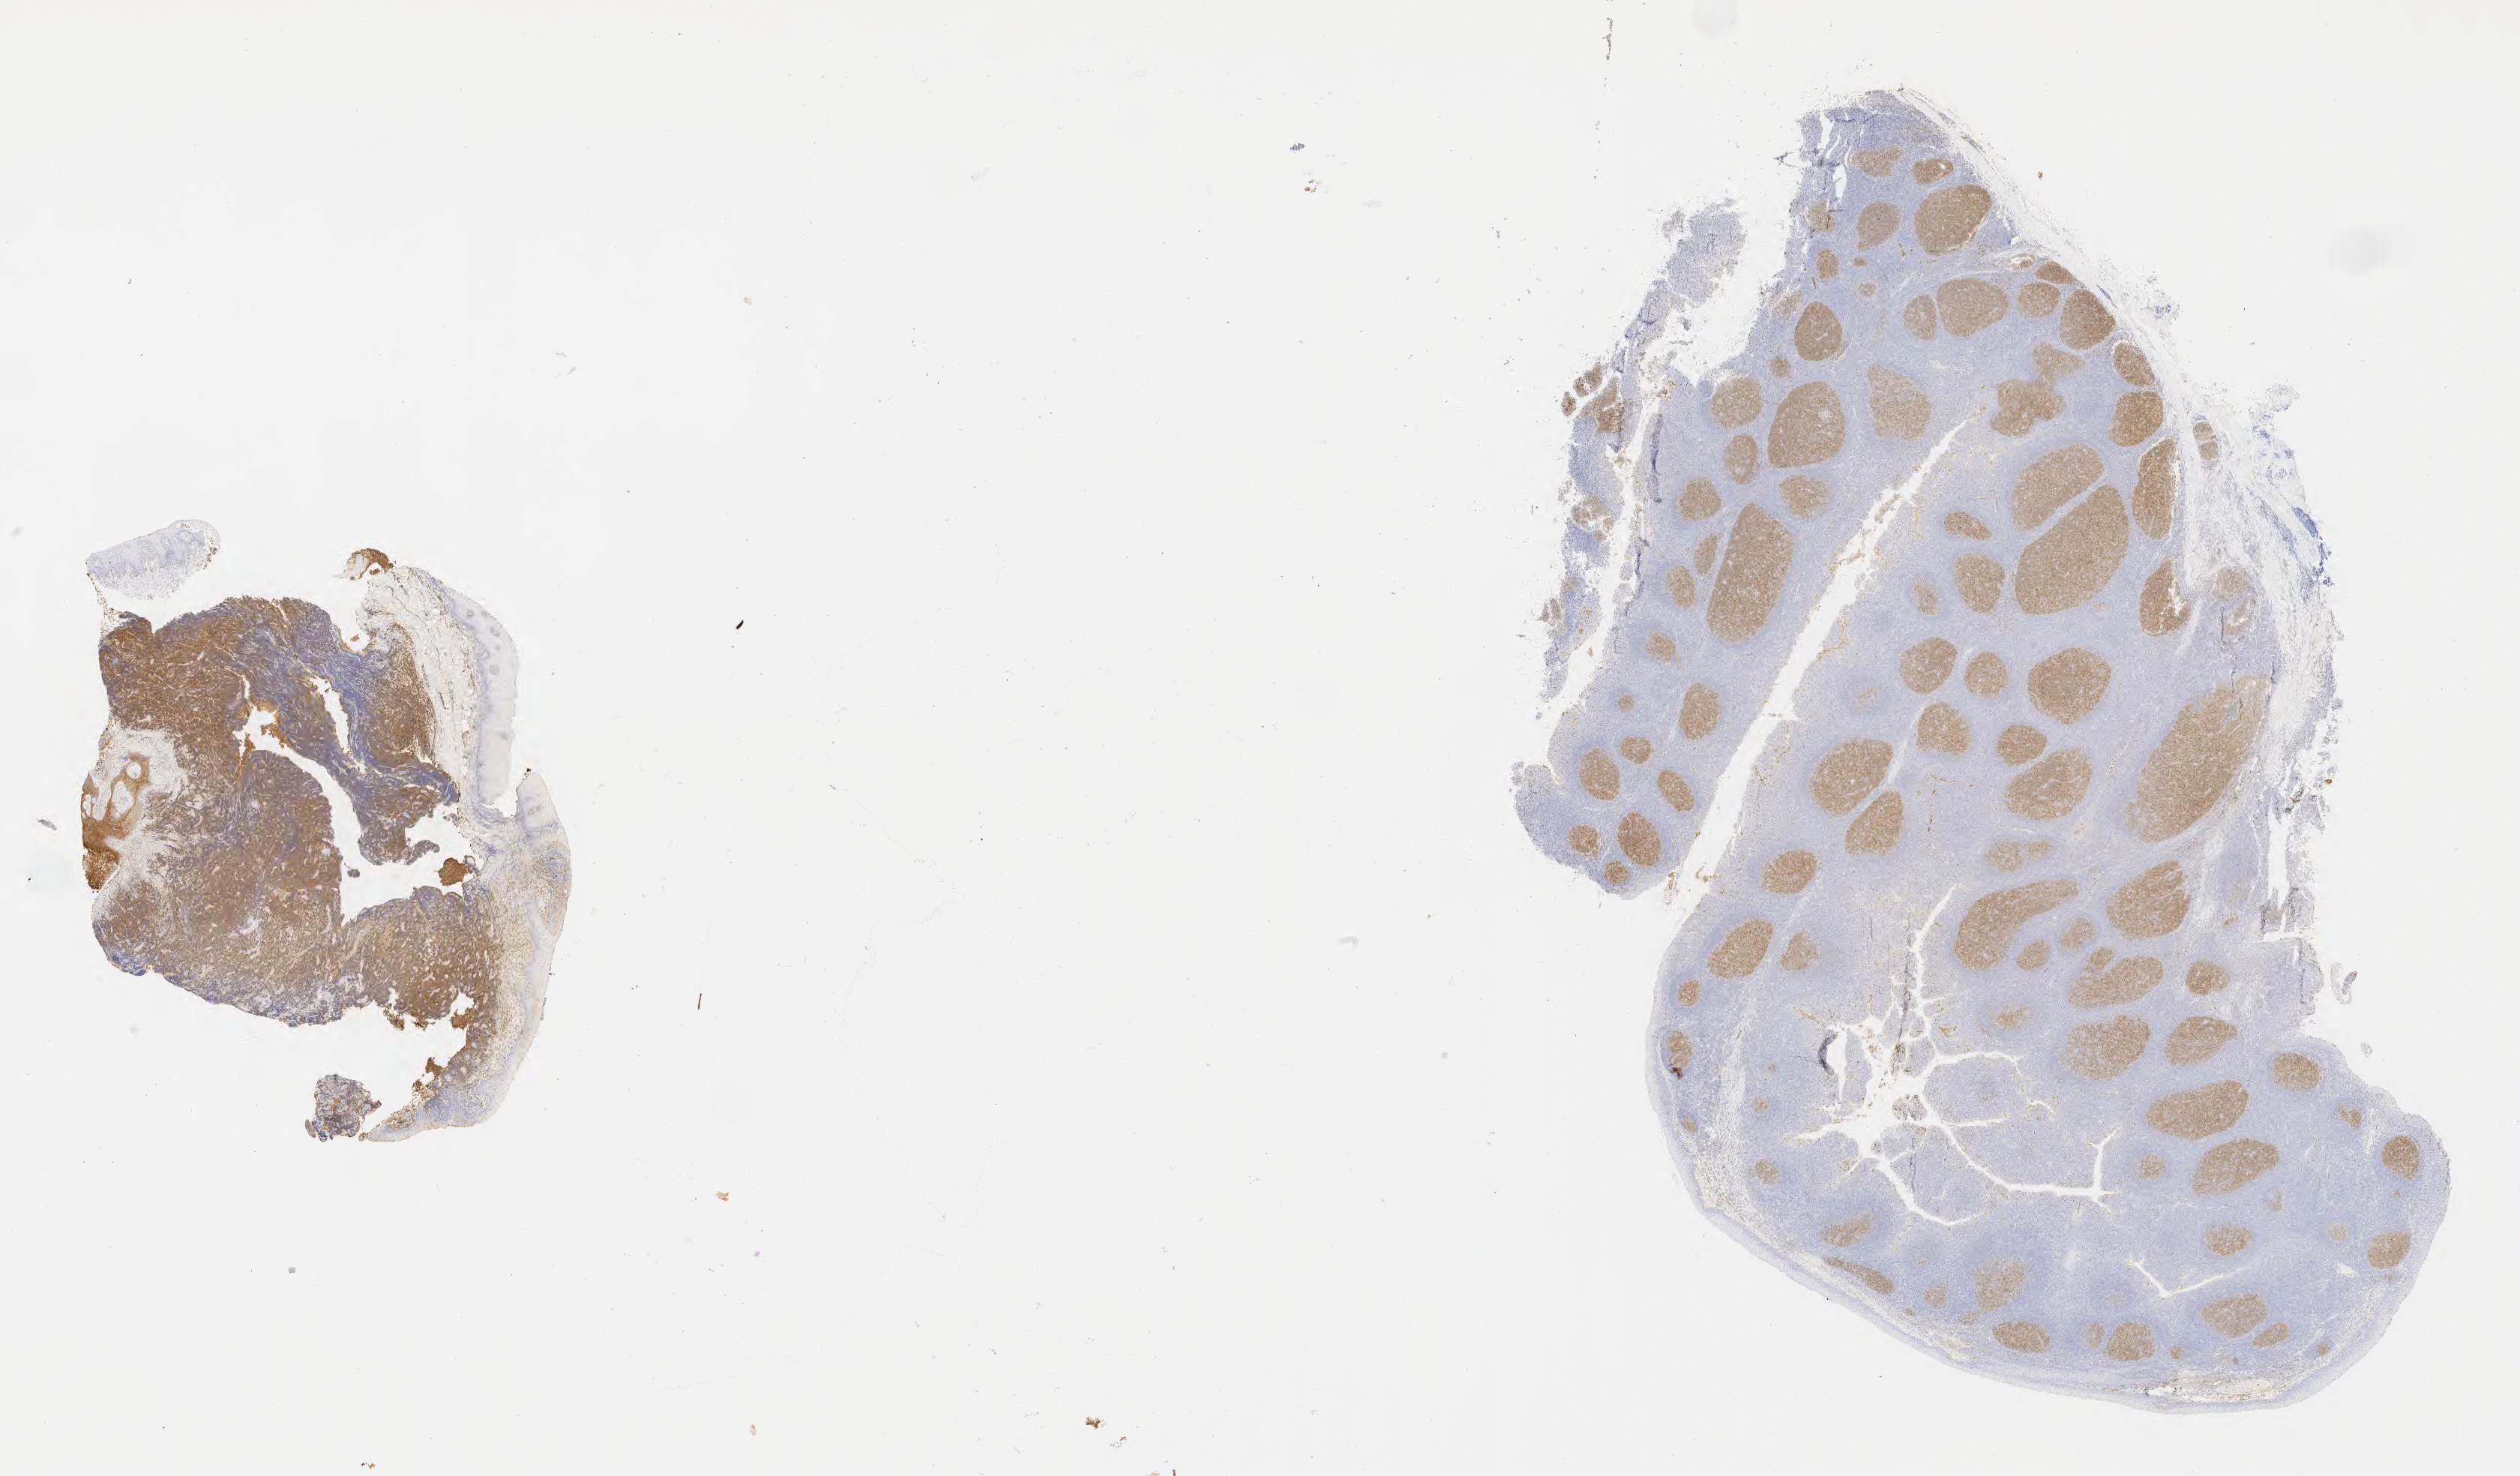
Immunohistochemistry (IHC) whole-slide image stained for CD10, shown as a low-resolution overview of the whole scanned area (about 27.2 x 15.9 mm), tumor tissue, site: mandible. Female patient; age at initial diagnosis 7 years.
Histologic diagnosis: Burkitt lymphoma, NOS.